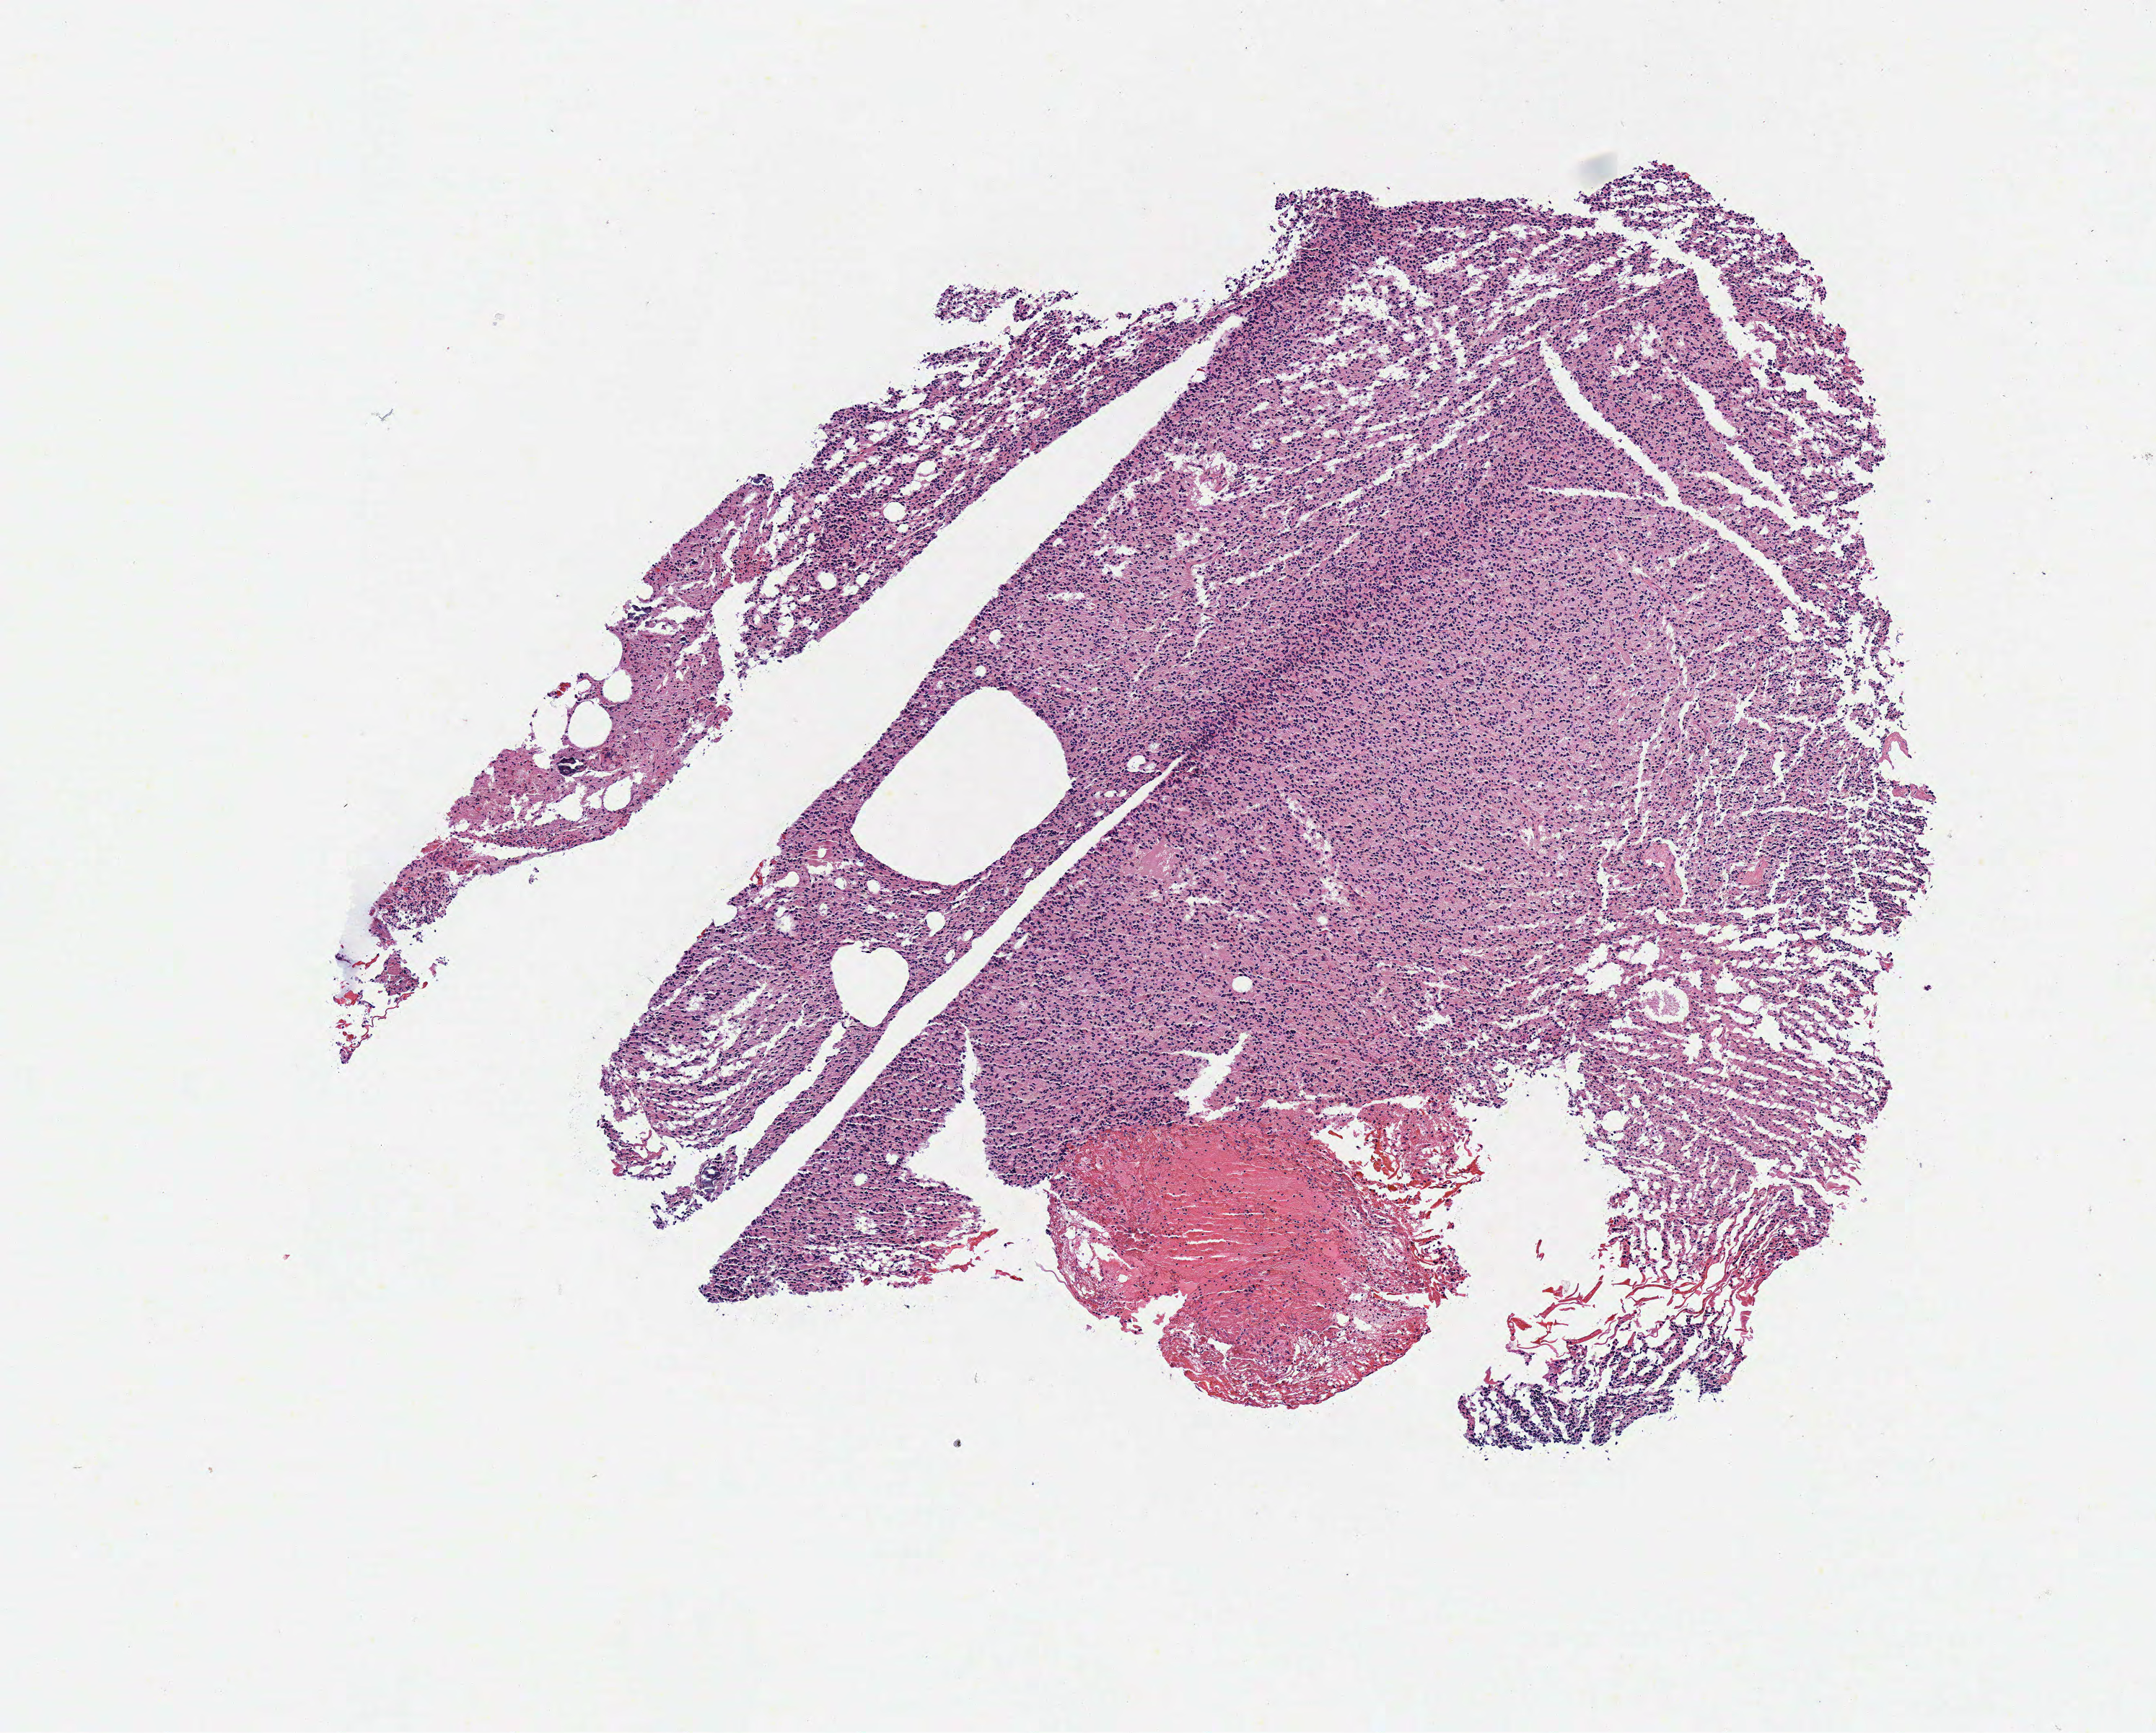
Digitized H&E tissue section (whole slide) — a low-resolution overview of the entire scanned area, about 5.9 x 4.7 mm (from a 40x scan), frozen section from the top of the tissue portion, brain, primary tumour sample. Patient: female, age at initial diagnosis 66 years. Histologic grade: G2 (moderately differentiated). Pathologist review of this section (percent, as recorded): tumour cells 100%, tumour nuclei 85%, normal cells 0%, stromal cells 0%, necrosis 0%.
• diagnosis: Oligodendroglioma, NOS